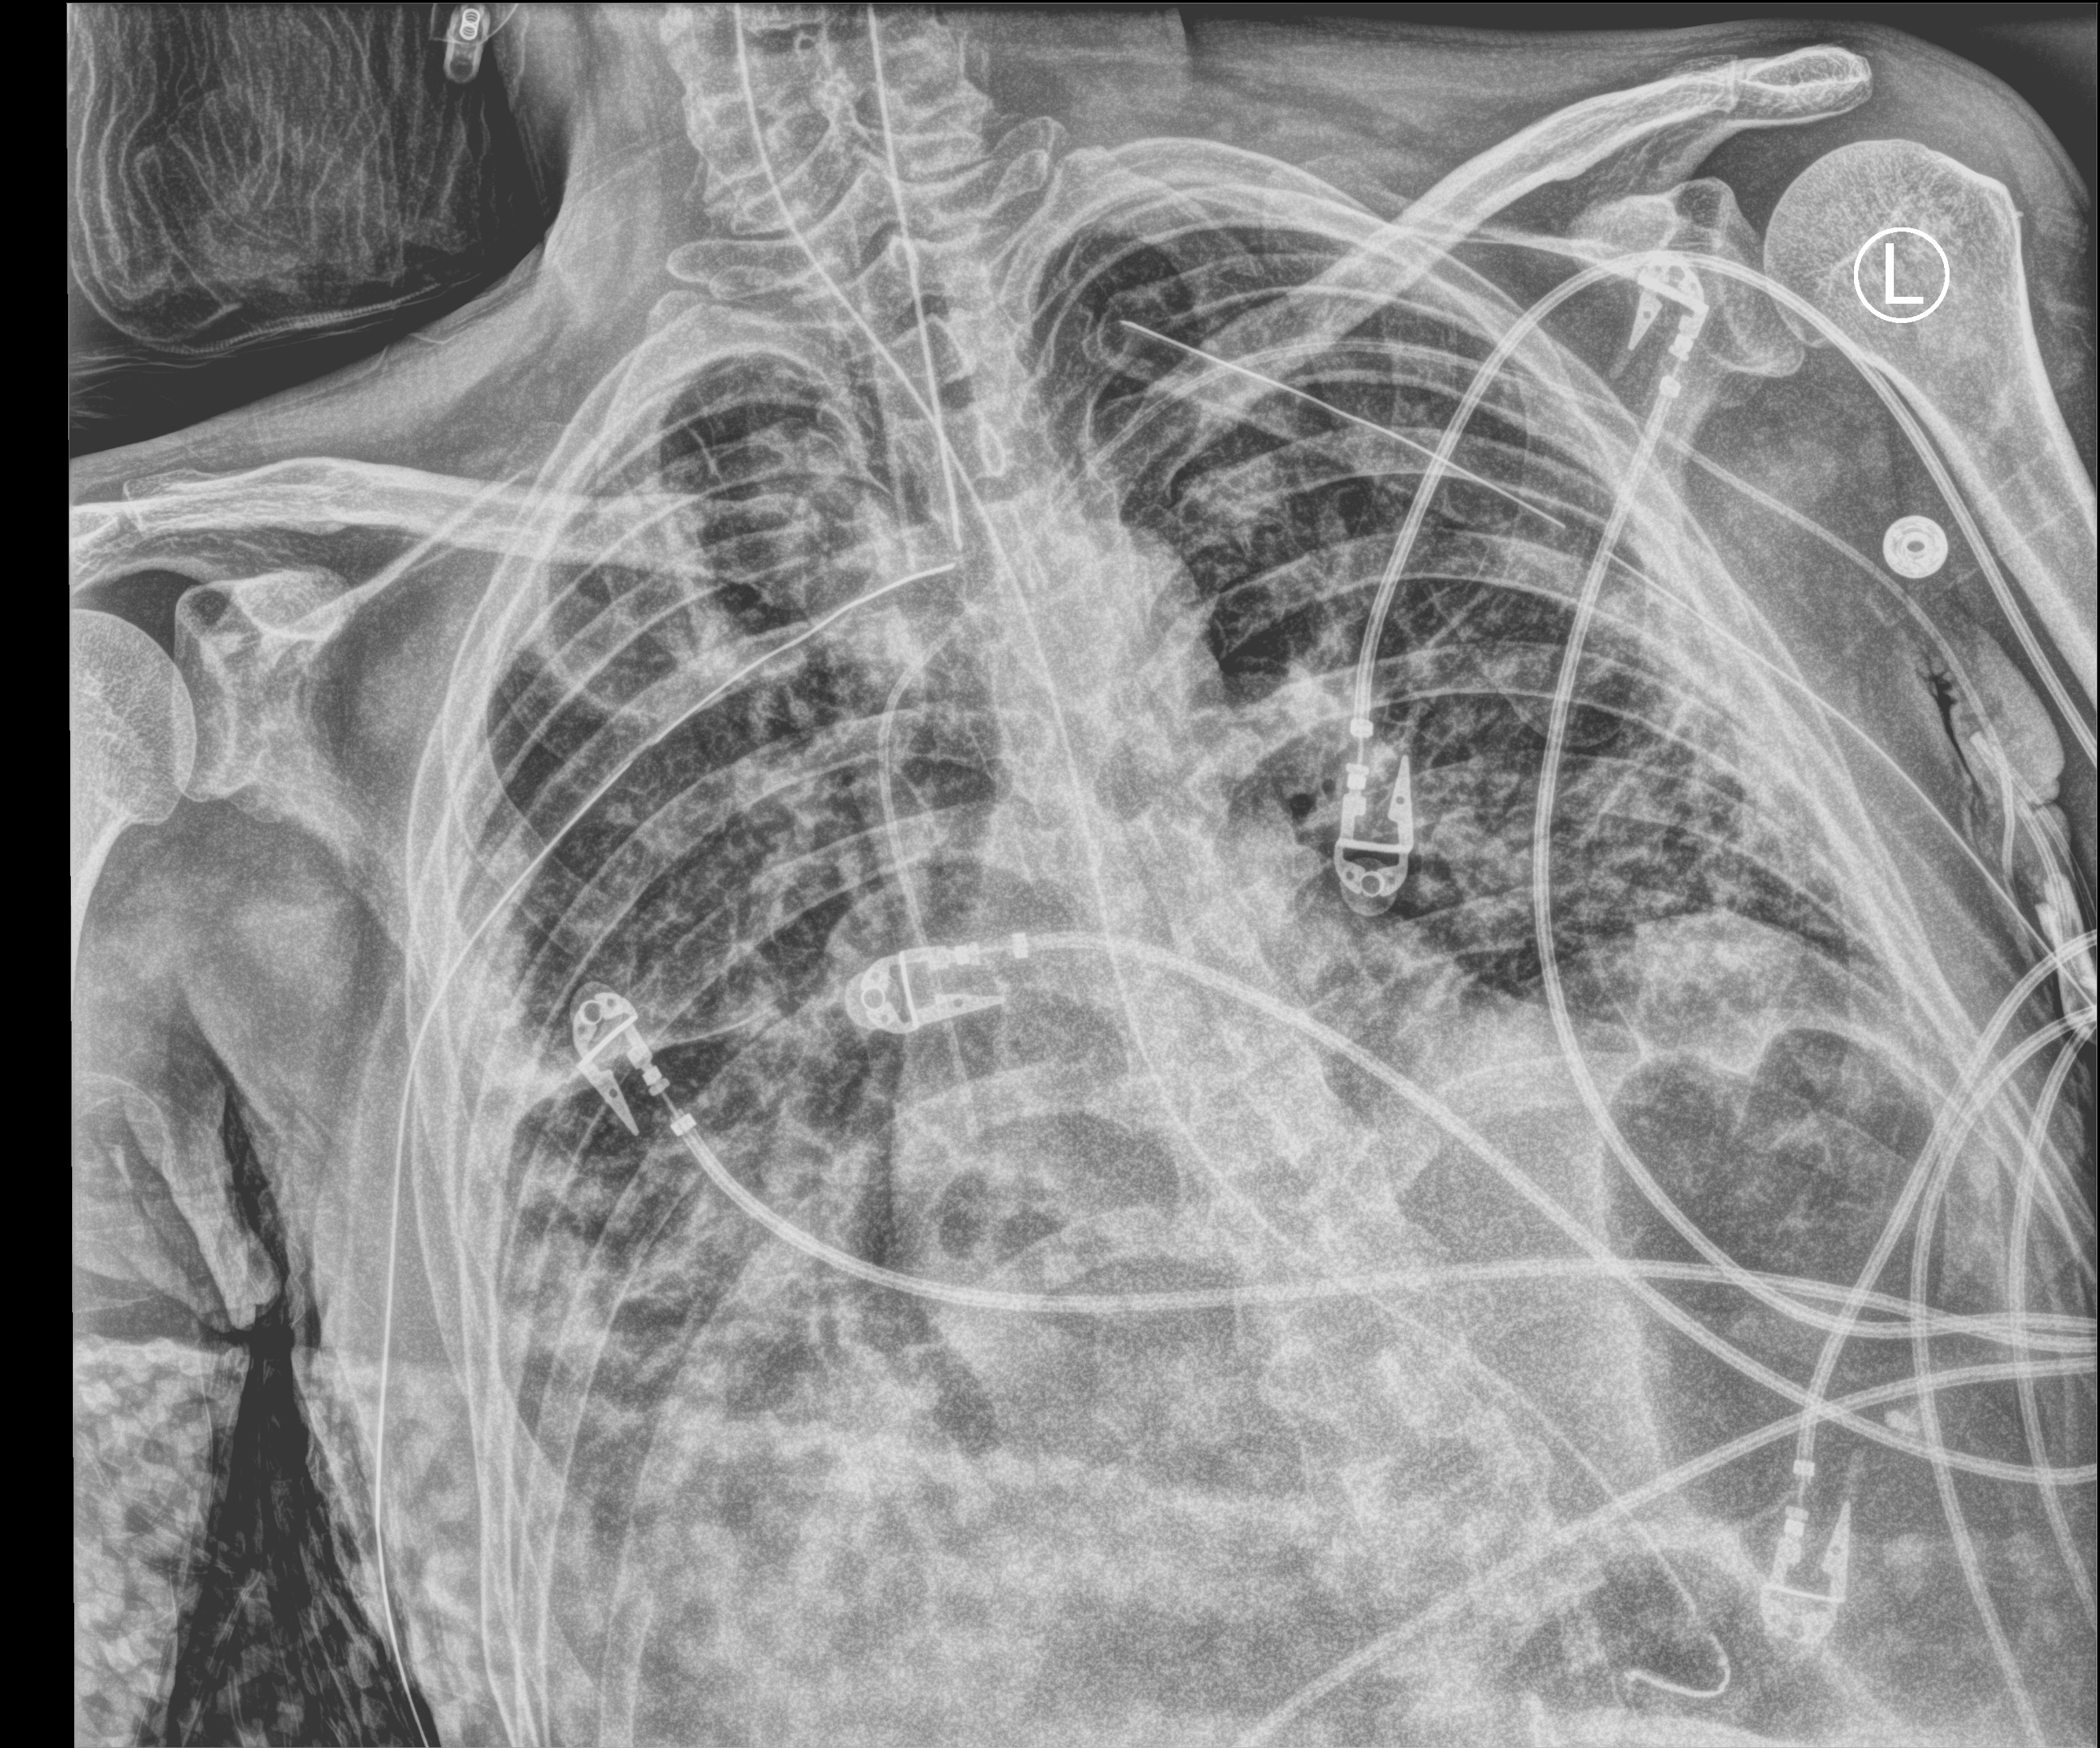
Portable chest radiograph, anteroposterior (AP) projection. Patient hospitalised with COVID-19; male, aged 18–59 years.
Admission-level facts for this patient (not findings on this image; timing relative to this image not recorded): mechanically ventilated during this hospital stay: yes.